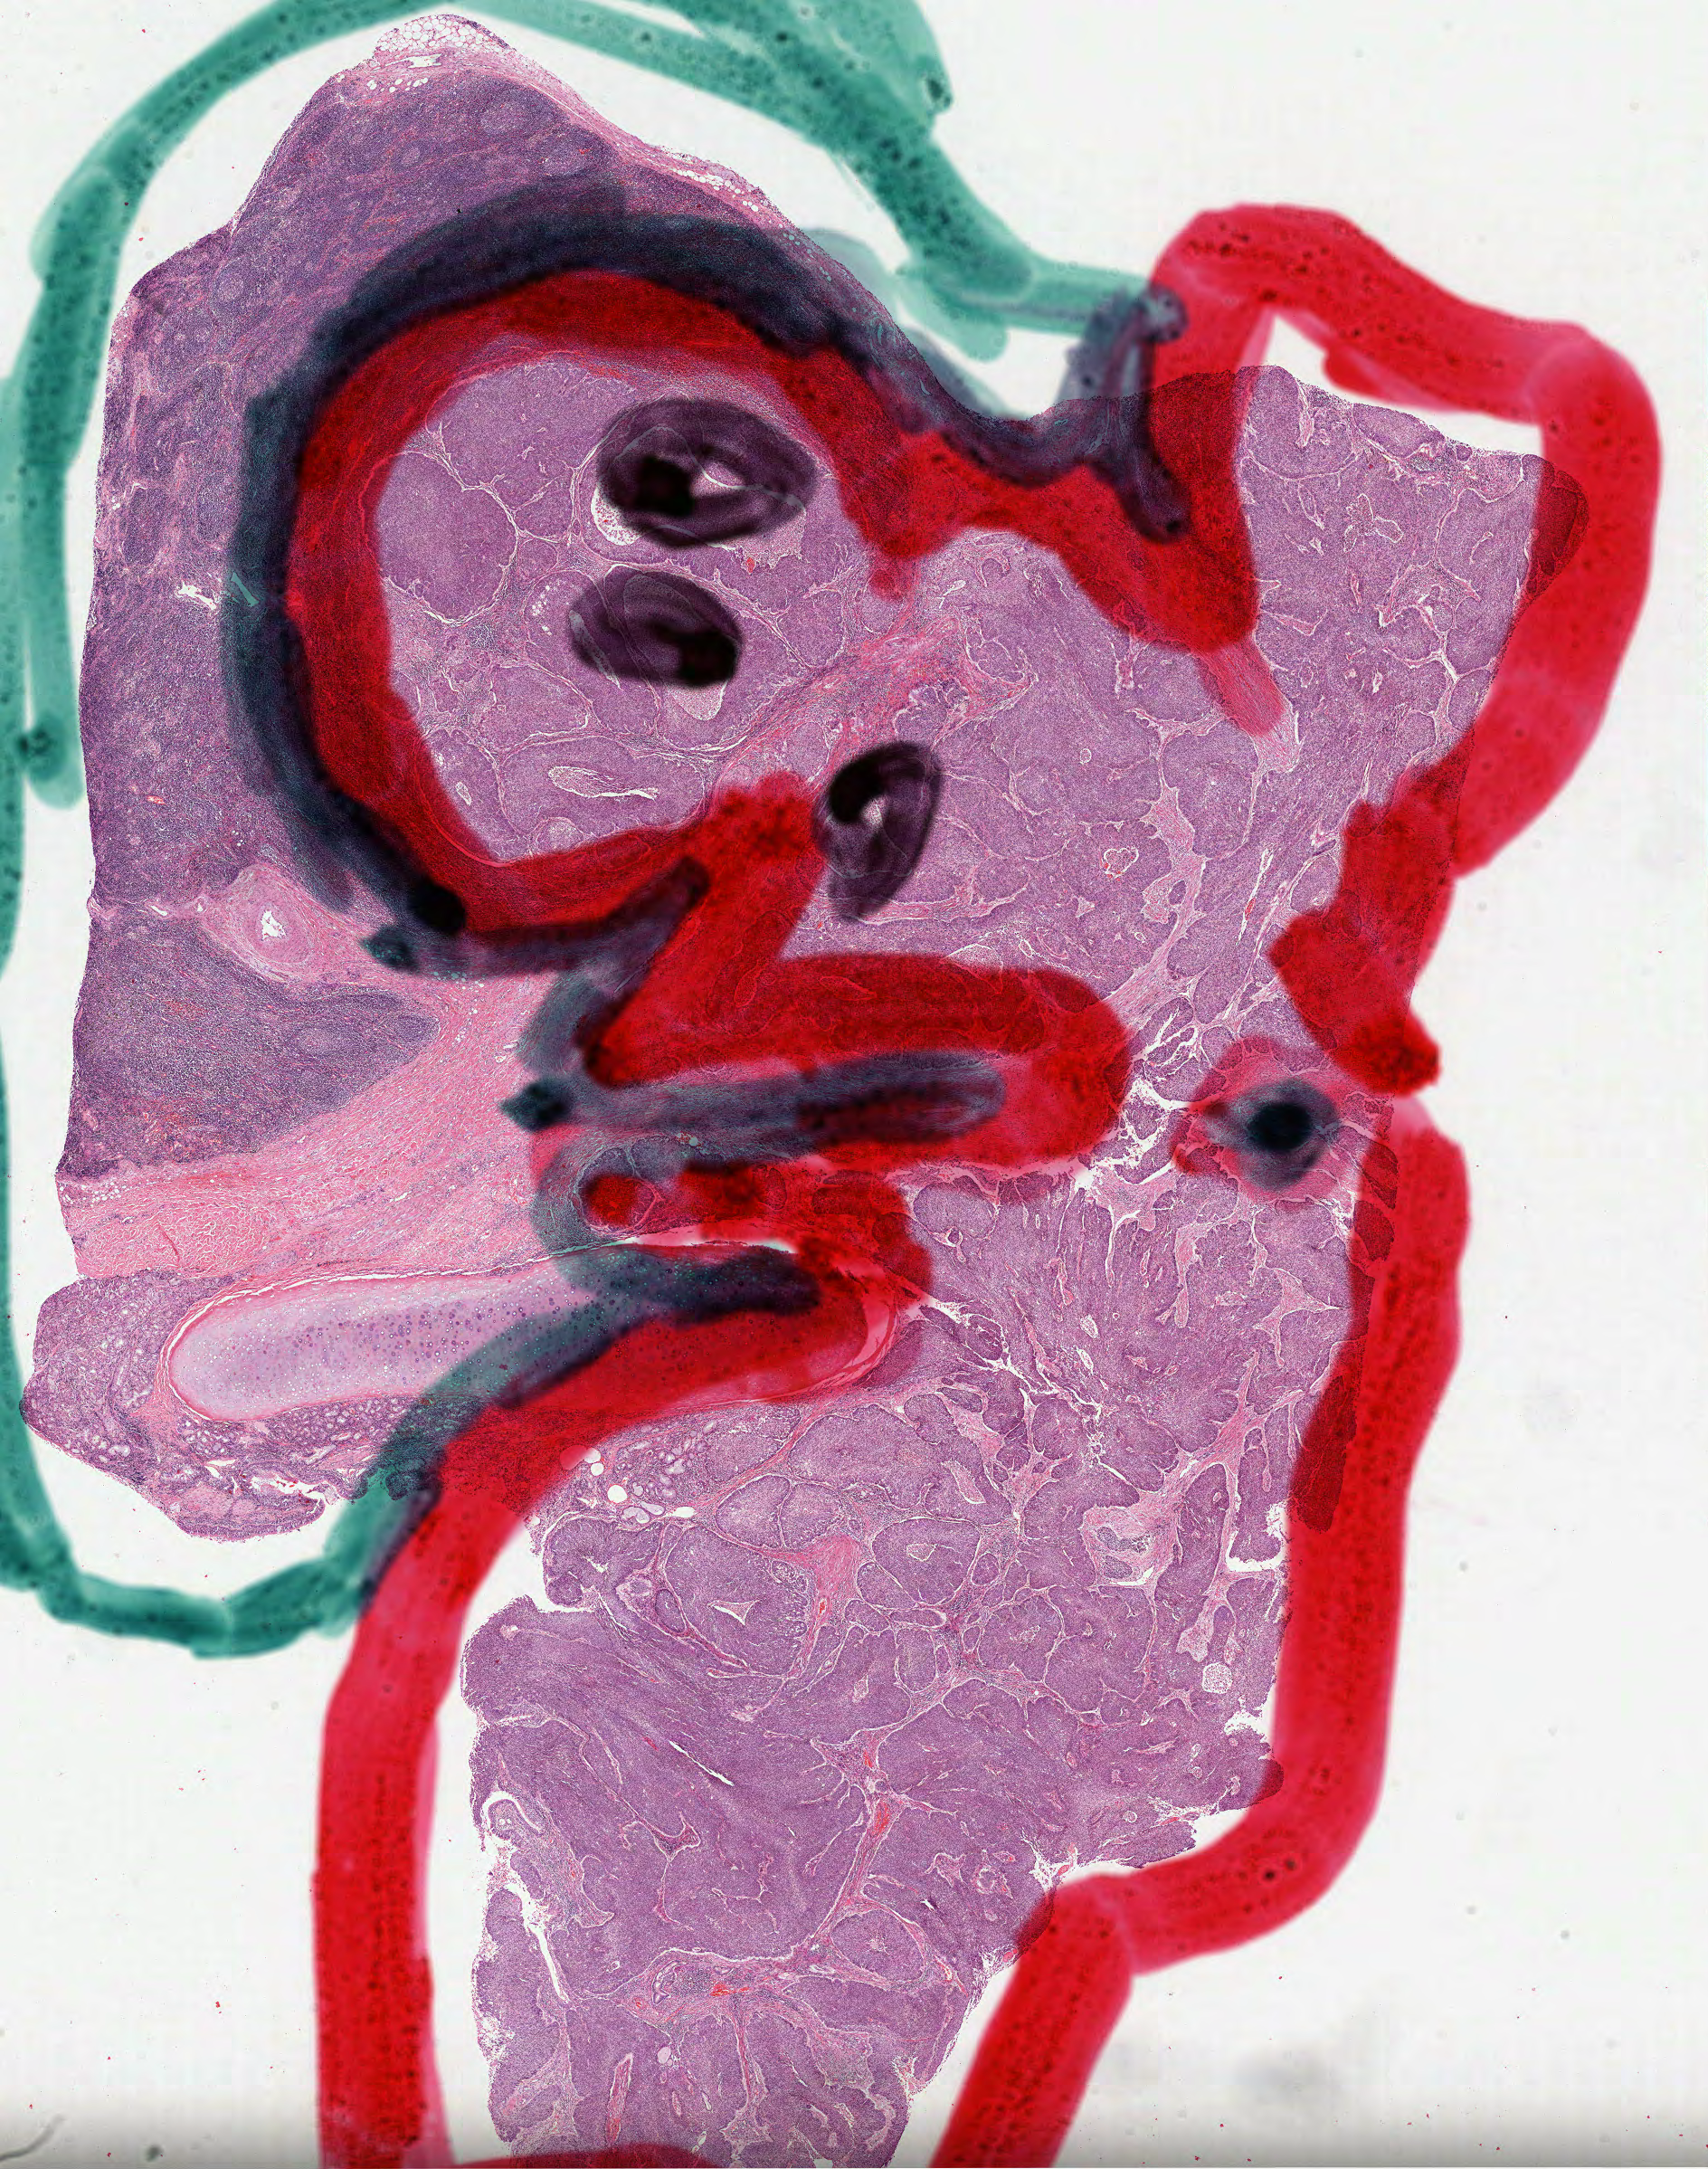
Digitized H&E tissue section (whole slide) — a low-resolution overview of the entire scanned area, about 15.2 x 19.3 mm (slide scanned at 40x); formalin-fixed paraffin-embedded (FFPE) diagnostic section; sample: primary tumour, lung. Male, age 52 years at initial diagnosis.
Histologic diagnosis: Squamous cell carcinoma, NOS (upper lobe, lung). AJCC pathologic stage: IIA (7th edition). Laterality: right.